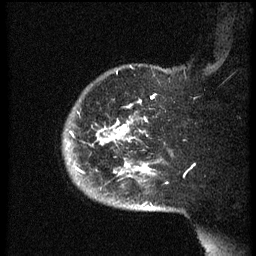
Breast MRI (dynamic contrast-enhanced), one sagittal slice; dynamic contrast-enhanced series, image 2 of 3 at this slice position (ordered by acquisition); 1.5 T; TE 4.2 ms, TR 8.4 ms; 2.5 mm slice thickness; 256 × 256 image matrix, field of view 200 × 200 mm. Female patient, age 38 years. Case-level facts recorded for this patient, not image findings: setting: breast cancer imaged before/during neoadjuvant chemotherapy; receptor status: HER2-positive.
Outlined on this slice (semi-automatic segmentation, software-assisted and operator-edited):
- analysis volume of interest (the breast-tissue region the enhancement analysis was run in; not a lesion): bounding box [x1, y1, x2, y2] px = [64, 74, 173, 202]
- tumour enhancement mask (voxels above the 70 % enhancement threshold inside the analysis volume of interest): [69, 119, 151, 176]